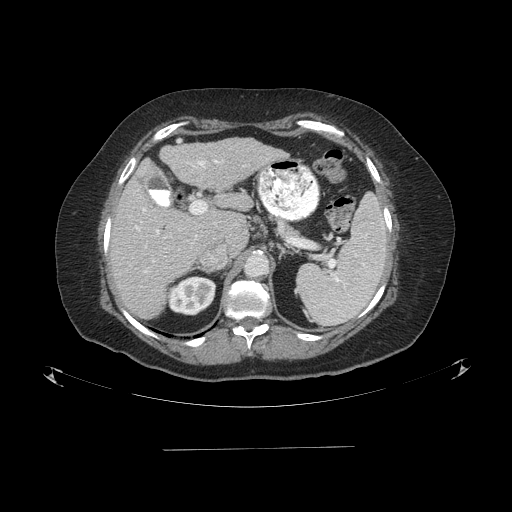
Contrast-enhanced abdominal CT (liver protocol), one axial slice. Slice 52 of 103 in the series (ordered by position). One of 2 acquisitions stored at this slice position. Soft-tissue window (W 400 / L 40 HU). 512 × 512 image matrix, field of view 500 × 500 mm. From the clinical record (not read from this slice): diagnosis: hepatocellular carcinoma (patient treated with transarterial chemoembolisation; whether this scan precedes or follows treatment is not stated here); TNM stage (as recorded): Stage-IIIA; Child-Pugh class: A; tumour differentiation: poorly differentiated; tumour nodularity: multinodular.
Outlined on this slice (semi-automatically segmented with operator editing):
- liver parenchyma outside the tumour (the mass and vessels are separate outlines, so this box may not span the whole liver): bounding box <110,138,287,318> (left, top, right, bottom; pixels)
- liver vessels: <135,160,219,273>